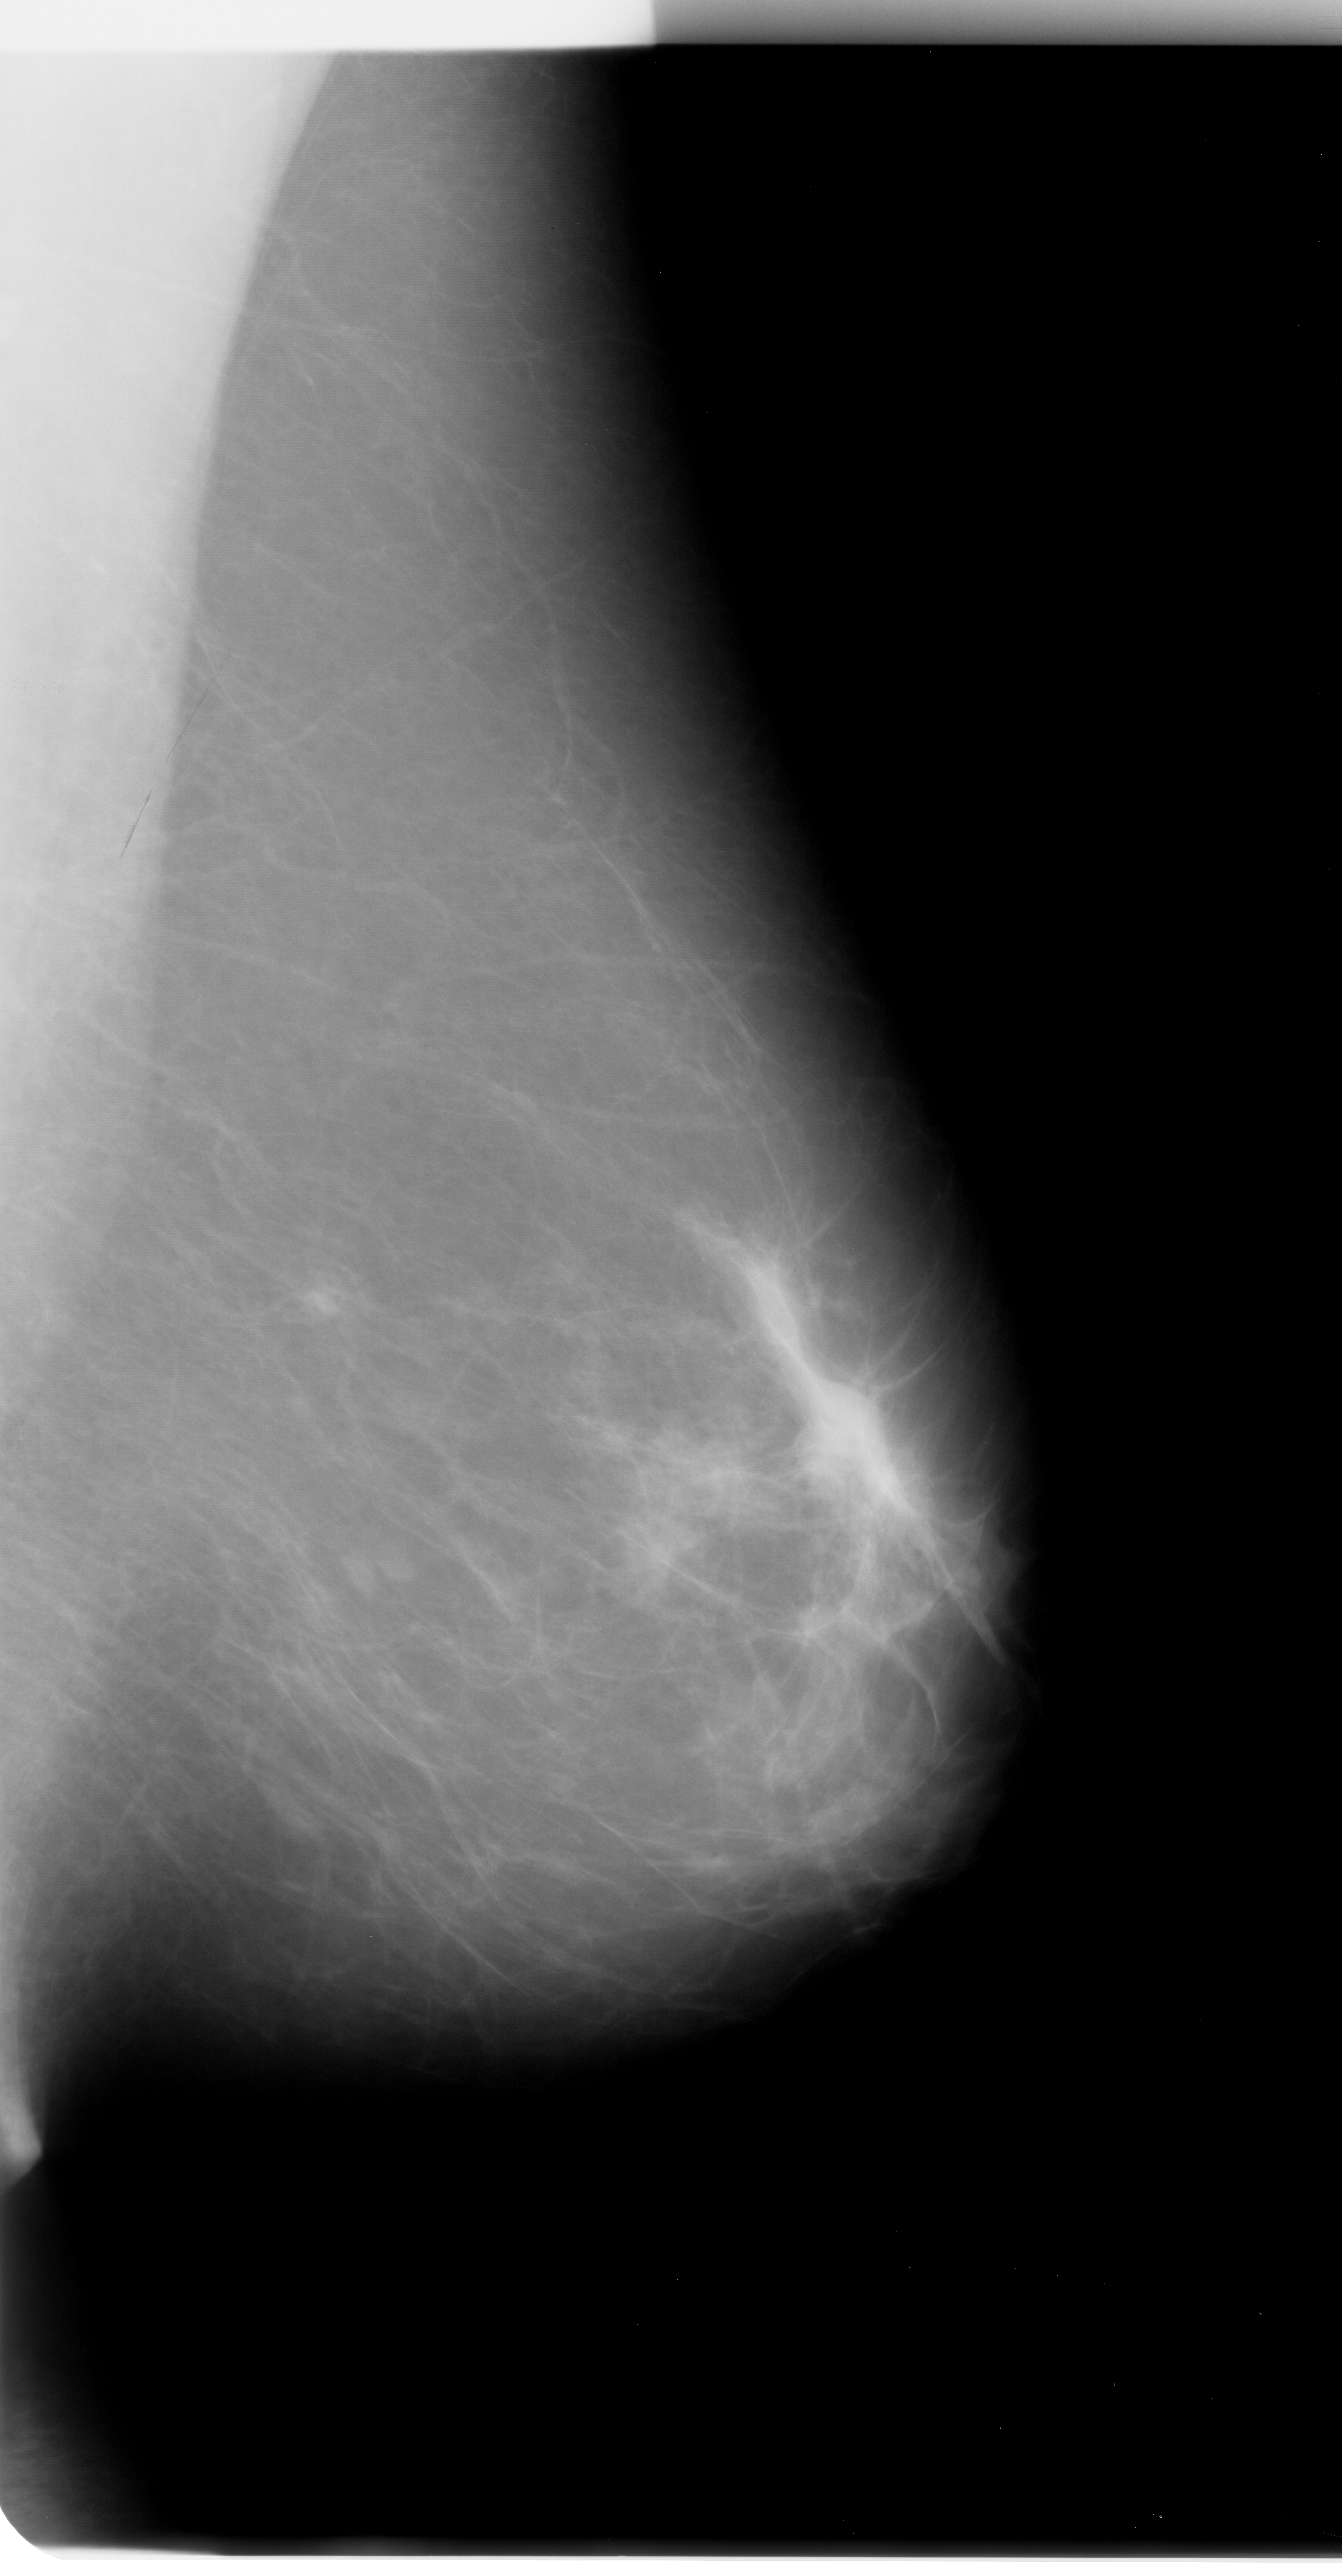
Mammogram (digitized film). Left breast. Mediolateral oblique (MLO) view. Breast composition: almost entirely fatty (BI-RADS density category 1 of 4). 1342 × 2576 image matrix.
Expert-marked regions of interest on this image (one box per marked abnormality):
- mass, shape lobulated, margins obscured; BI-RADS assessment category 3; subtlety rating 3 on a 1 (subtle) to 5 (obvious) scale; pathology (as recorded): malignant: bounding box [x1, y1, x2, y2] px = [783, 1363, 903, 1491]